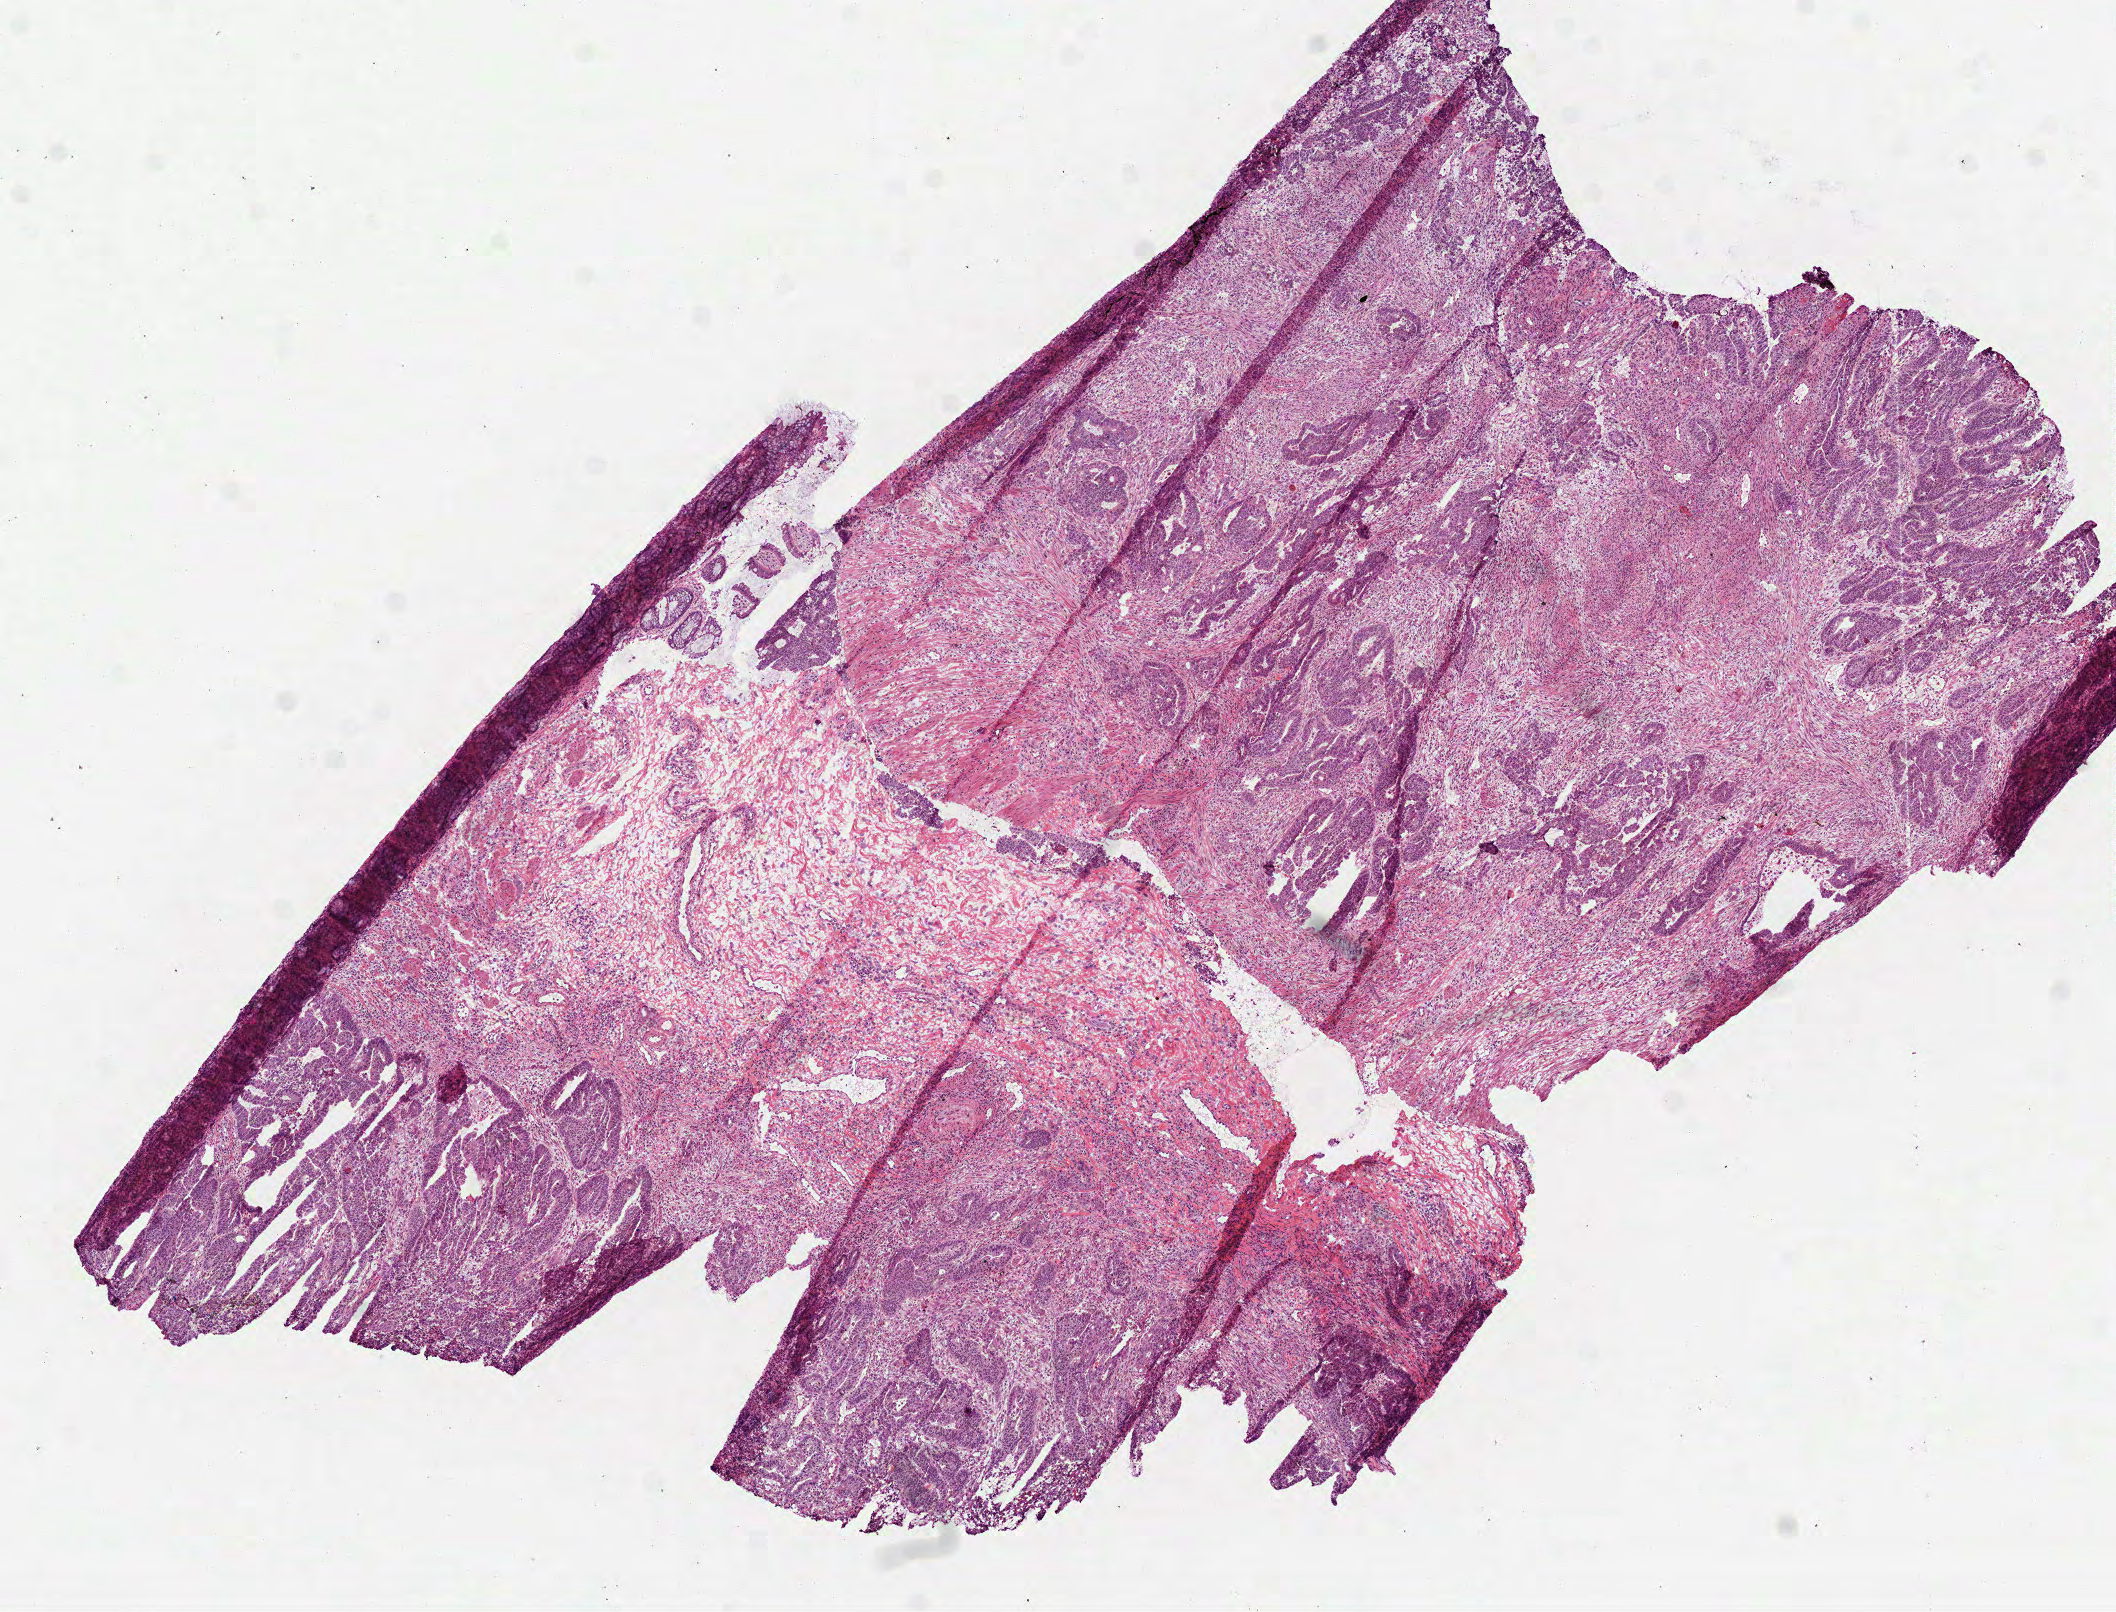
Digitized H&E-stained tissue section (whole slide) — a low-resolution overview of the entire scanned area, about 8.5 x 6.5 mm (acquisition: 40x scan); frozen section from the top of the tissue portion; primary tumour sample from the rectum. Male patient; age at initial diagnosis 66 years. Slide review estimates, as recorded: tumour cells 78%, tumour nuclei 60%, normal cells 1%, stromal cells 20%, necrosis 1%. Inflammatory infiltration, as recorded: lymphocyte infiltration 15%, monocyte infiltration 2%, neutrophil infiltration 15%.
TNM: T2 N1 M0. AJCC pathologic stage: IIIA (7th edition). Pathologic diagnosis: Adenocarcinoma, NOS (rectosigmoid junction). Lymph nodes positive (case pathology): 2 of 29 examined.